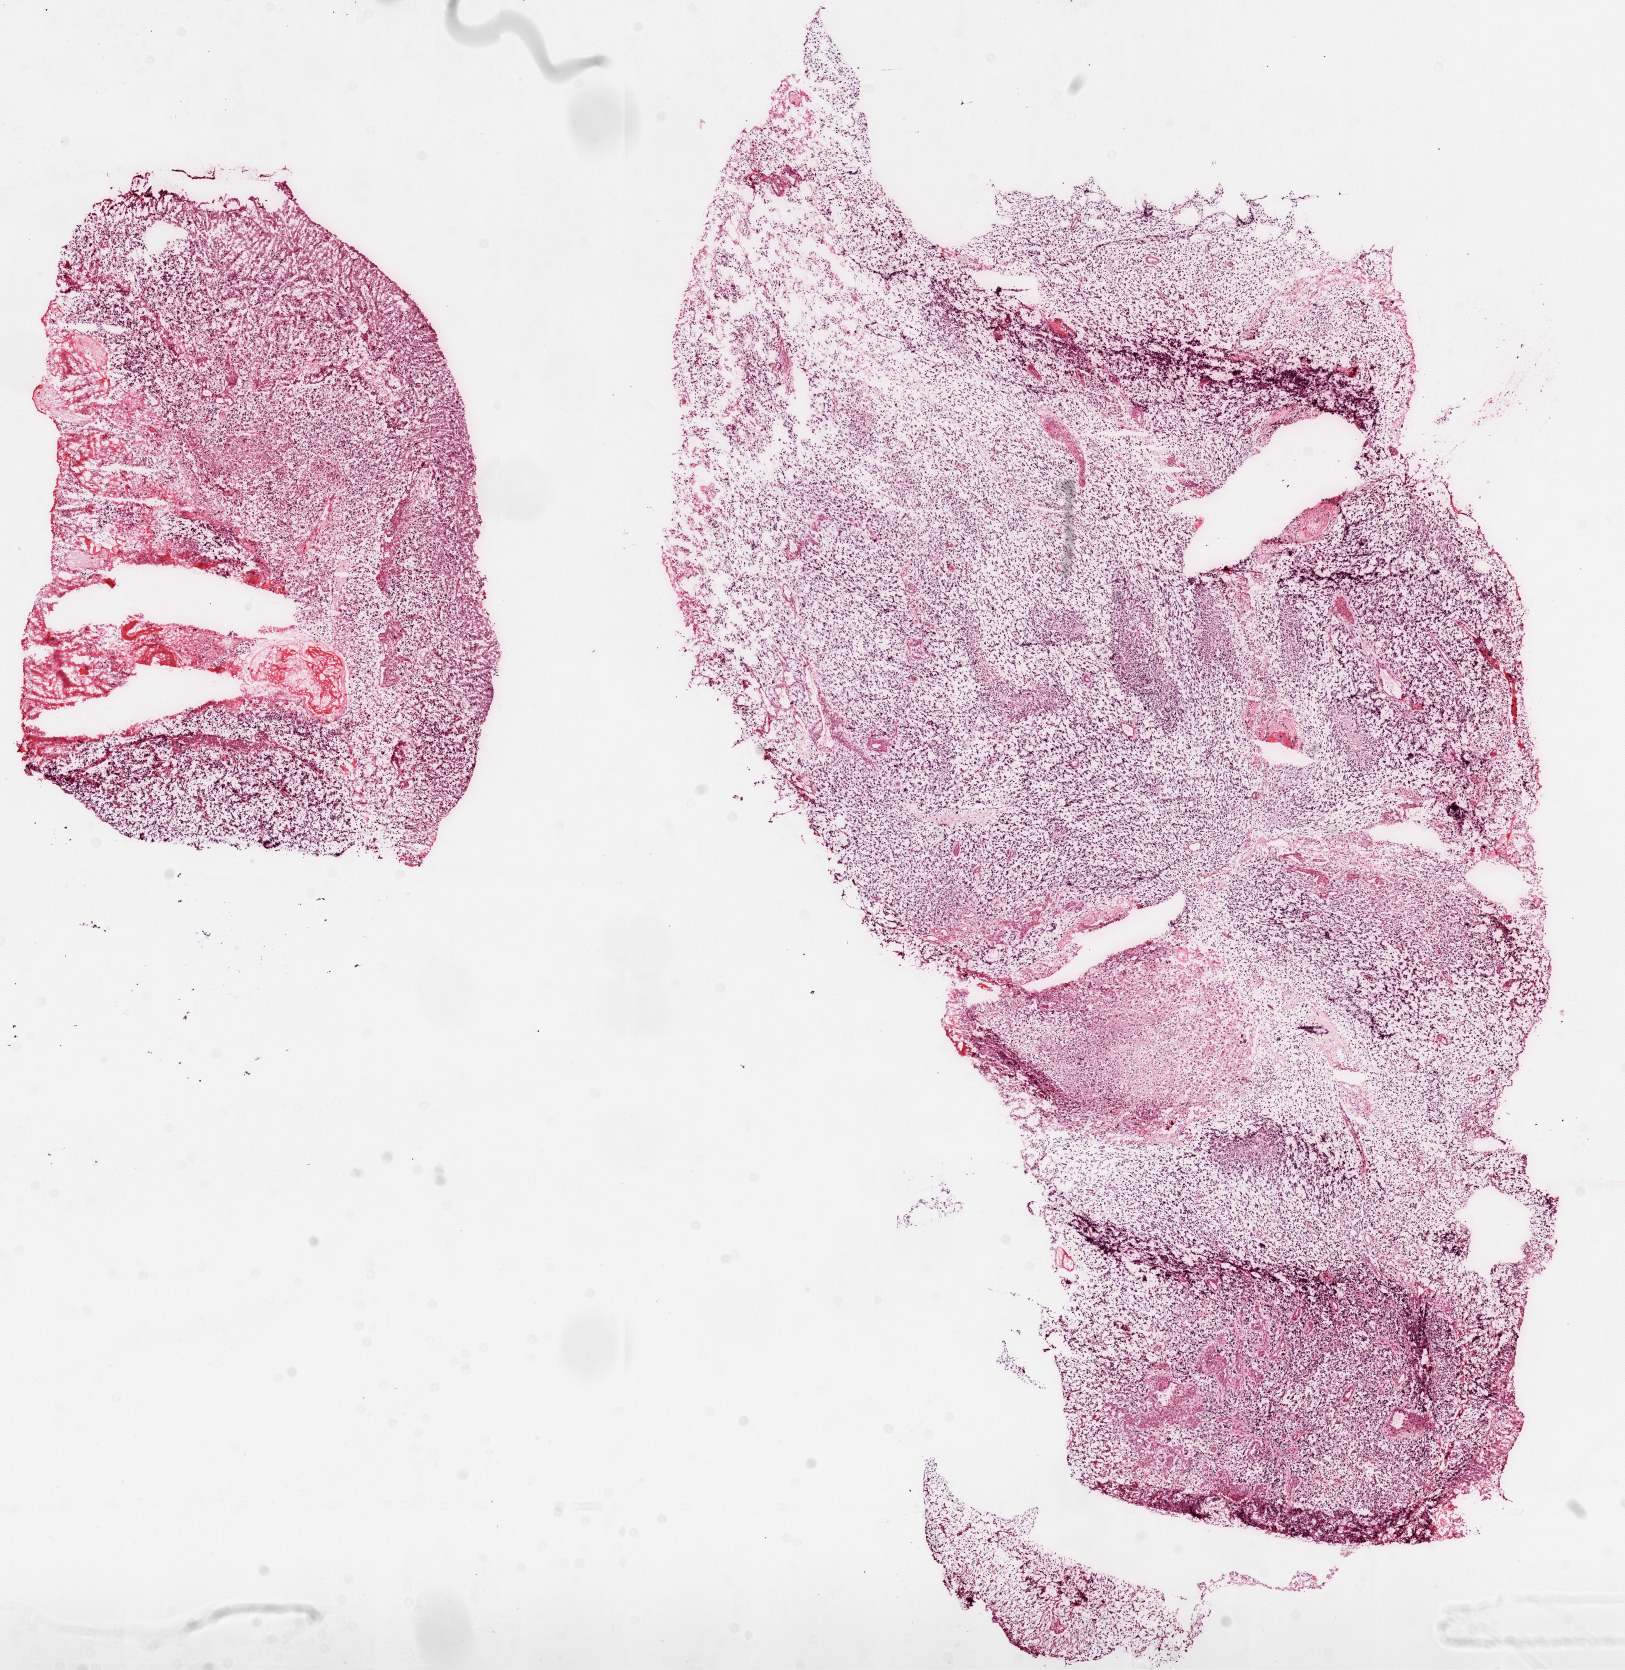
H&E whole-slide image — shown as a low-resolution overview of the whole scanned area (about 13.0 x 13.4 mm, from a 20x scan). Frozen section from the top of the tissue portion. Brain, primary tumour sample. Female, age 54 years at initial diagnosis. Pathologist review of this section (percent, as recorded): tumour cells 85%, tumour nuclei 100%, normal cells 0%, stromal cells 0%, necrosis 15%.
Diagnosis: Glioblastoma.